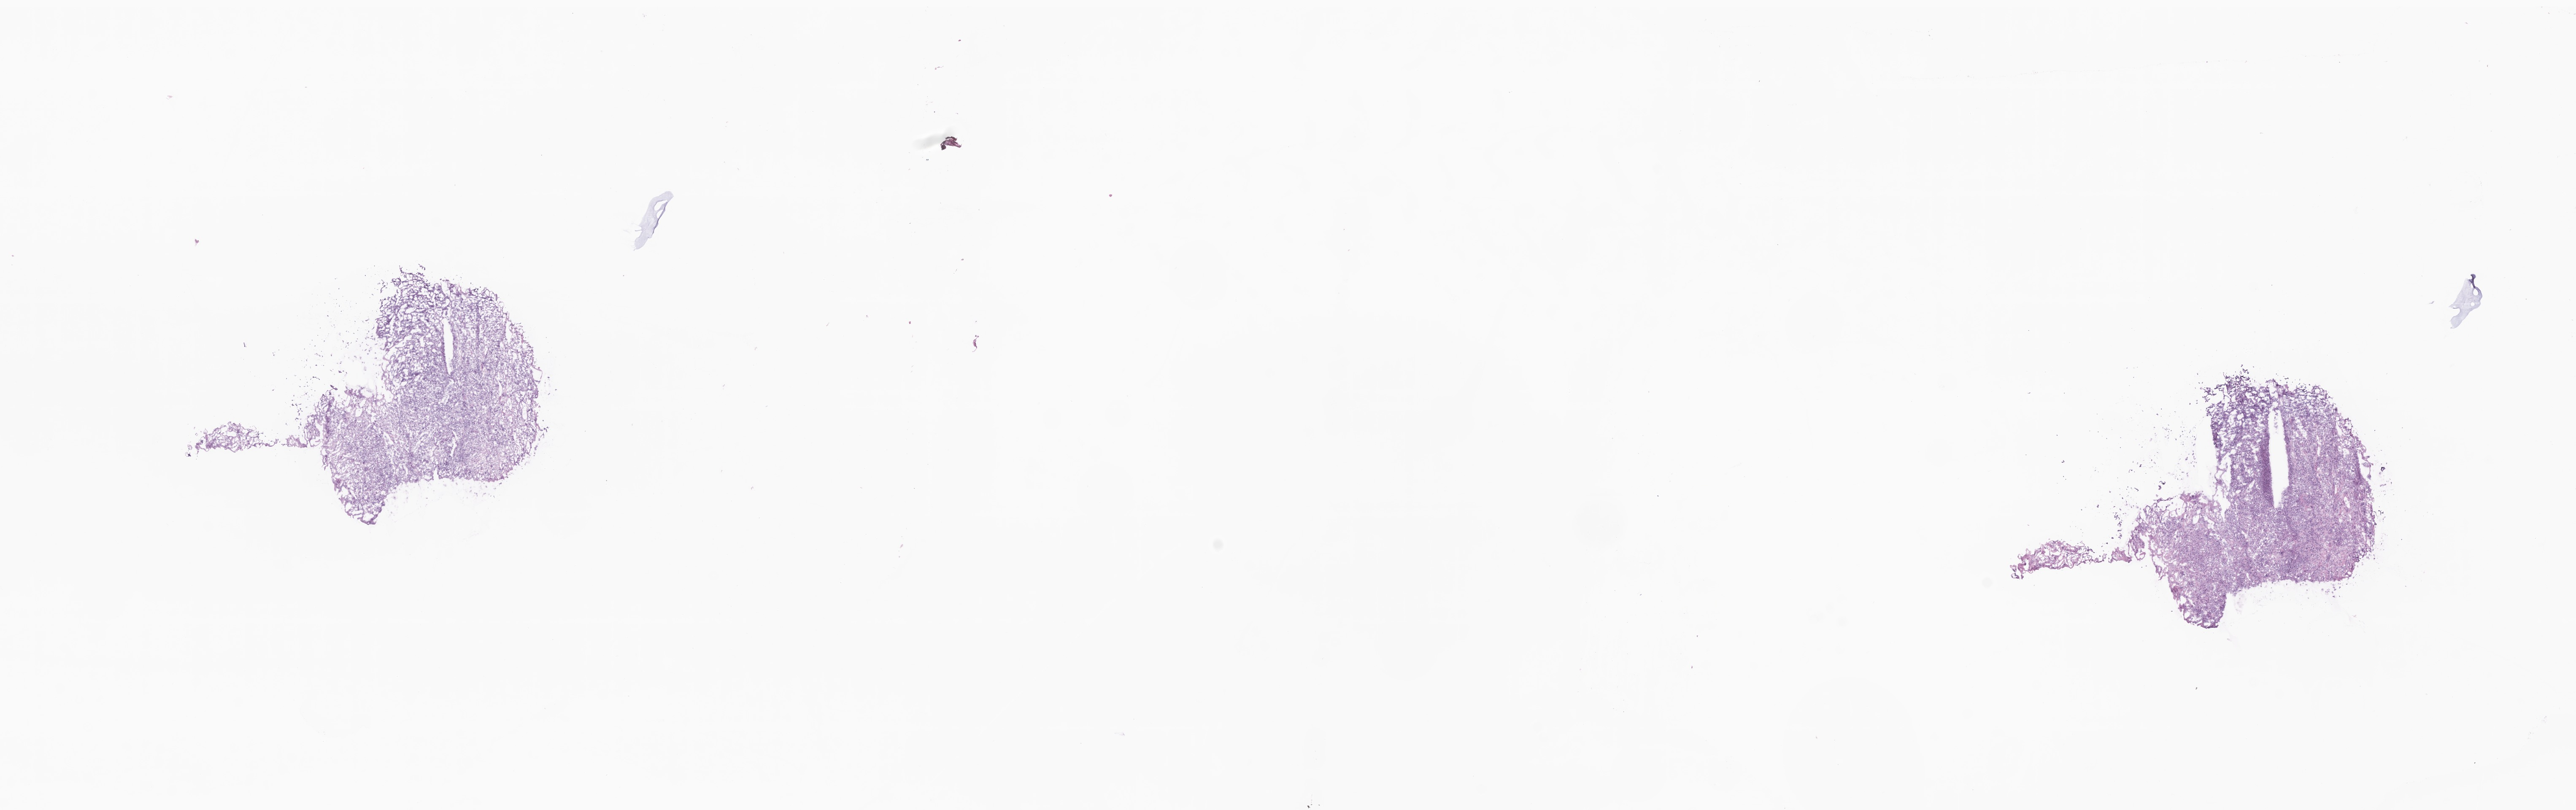
H&E whole-slide image, low-resolution overview of the scanned area, about 25.7 x 8.1 mm, frozen section (tissue freezing medium), specimen: metastatic tumor tissue. Patient: male, age at initial diagnosis 82 years. Pathologist review of this section (percent, as recorded): tumor cells 100%, tumor nuclei 90%, stromal cells 0%, necrosis 0%, normal cells 0%. Inflammatory infiltration, as recorded: lymphocyte infiltration 0%, monocyte infiltration 0%, neutrophil infiltration 0%.
Section: bottom of the tissue portion. Patient diagnosis (primary): Adenocarcinoma, NOS.